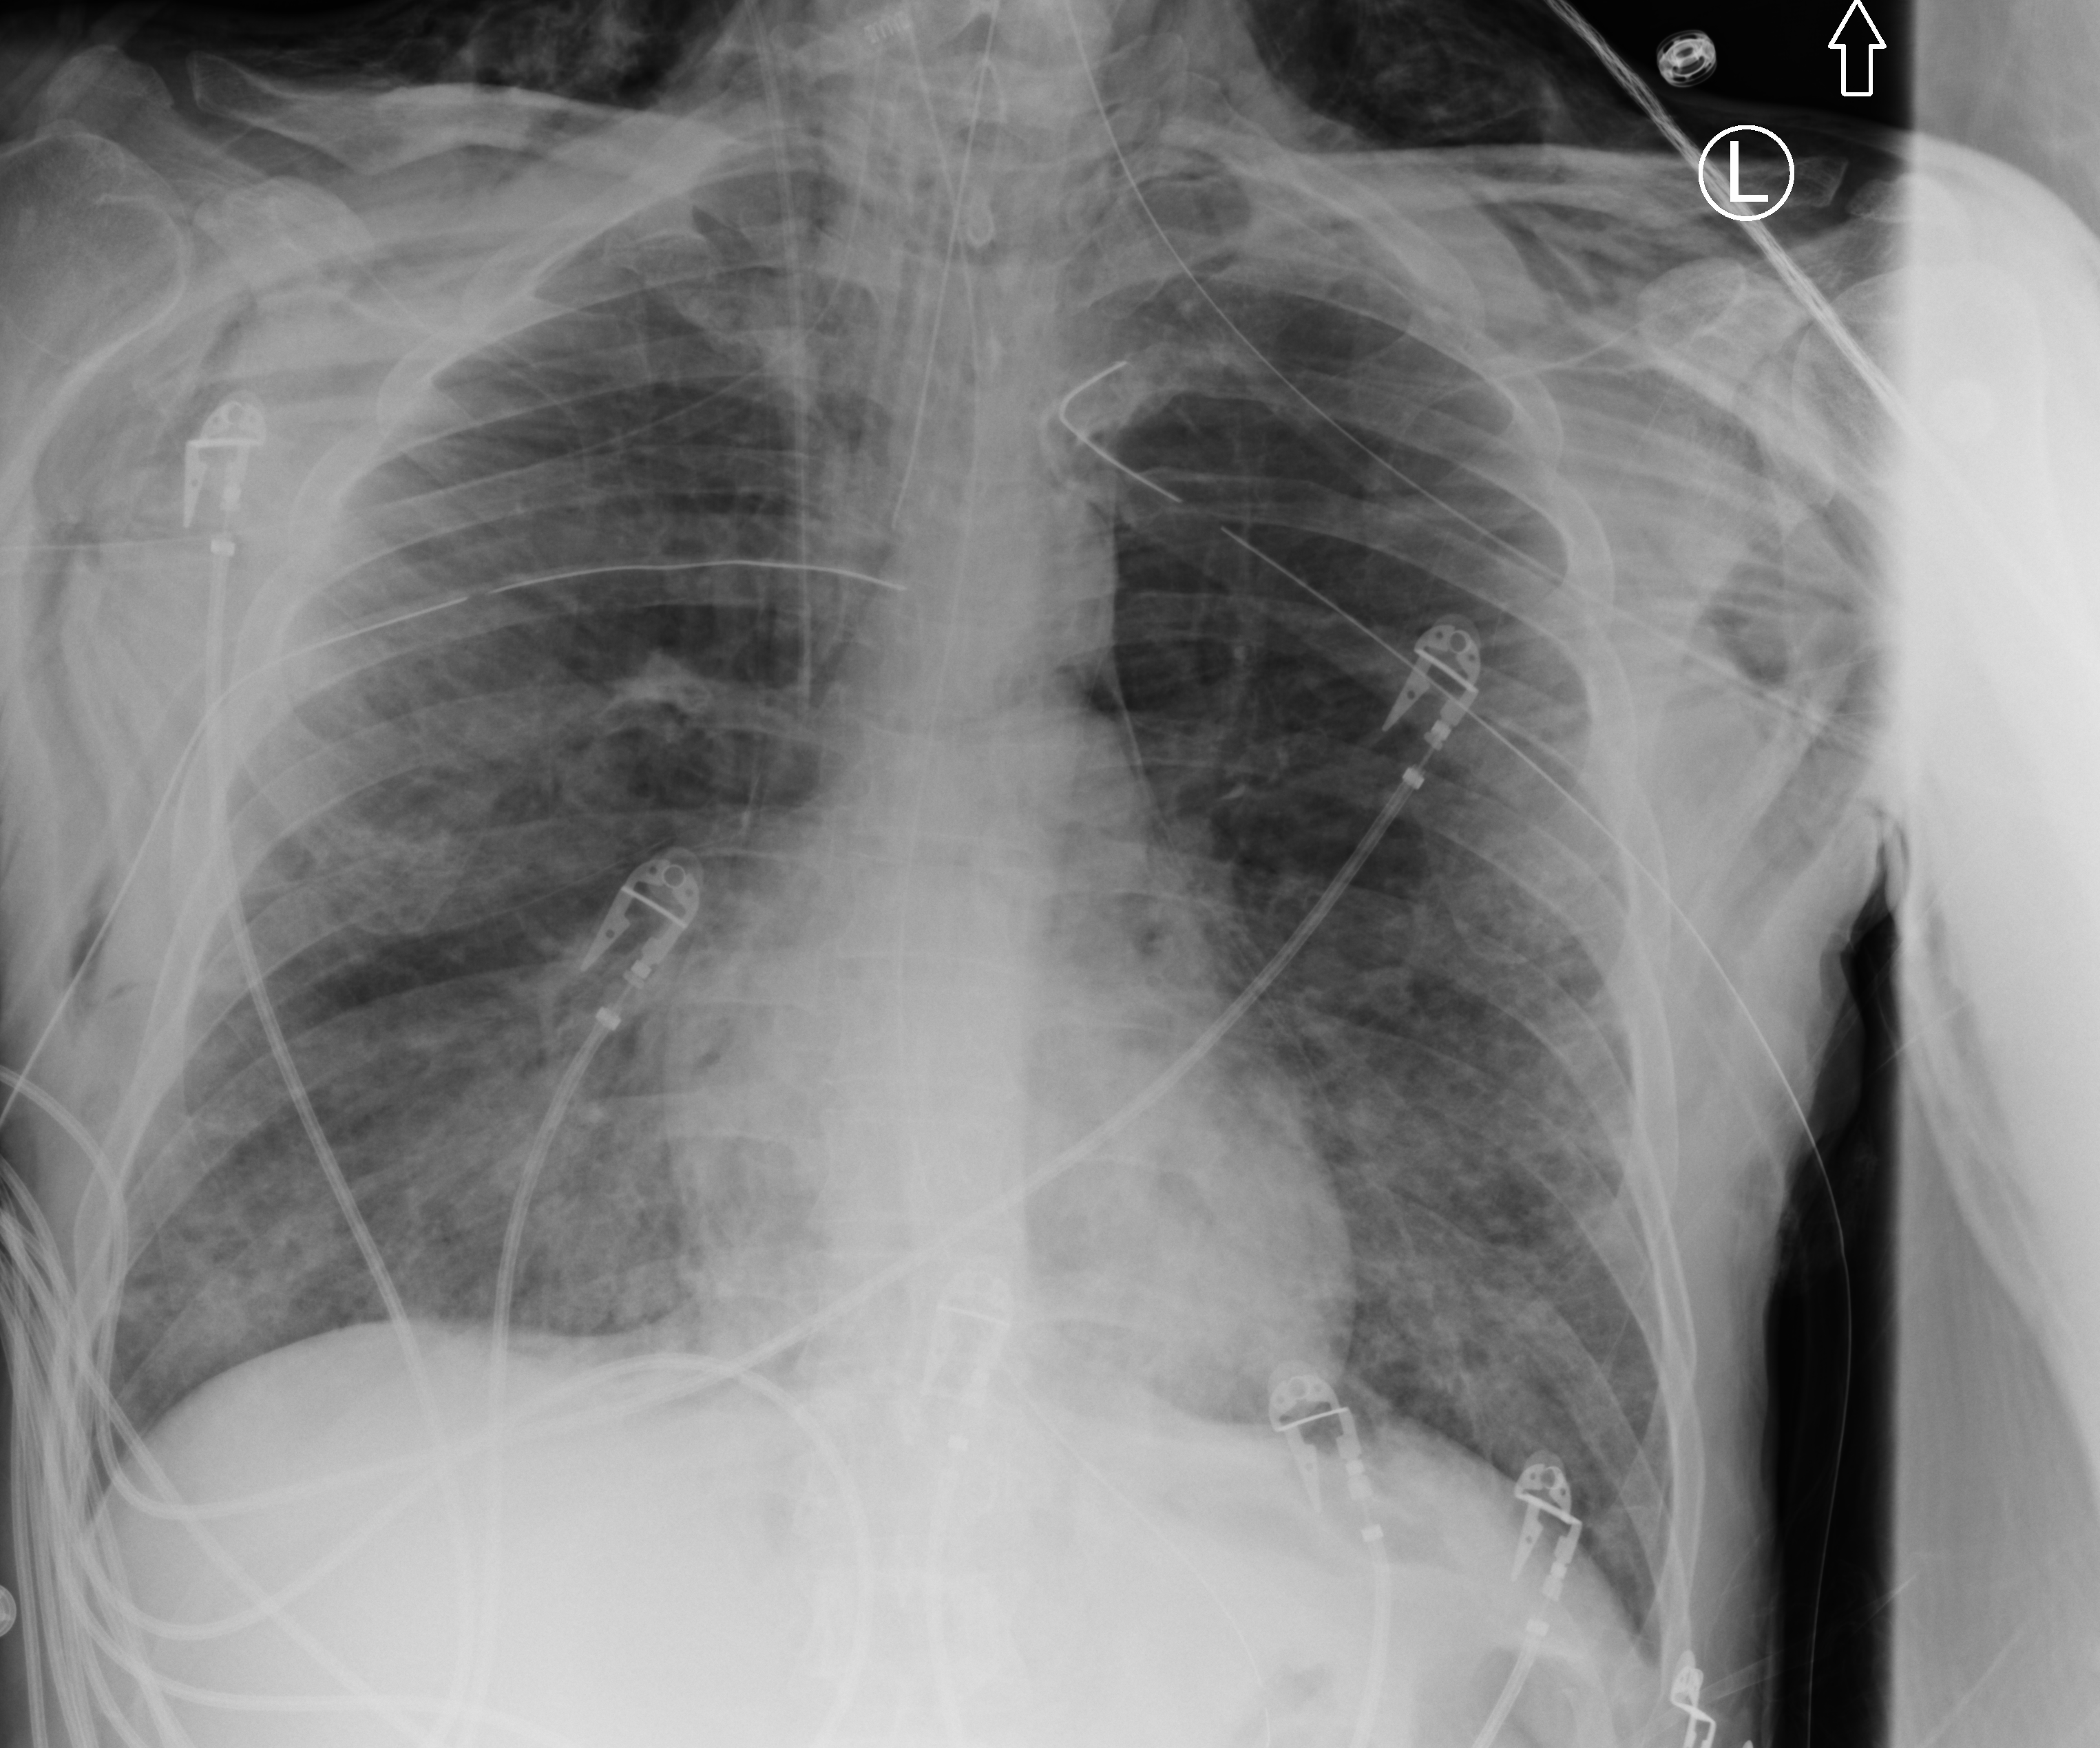
Portable chest radiograph, anteroposterior (AP) projection. Male patient hospitalised with COVID-19, age 18–59 years.
From the hospital-stay record, not from the radiograph (when in the stay this image was taken is not recorded): COPD (admission record): no; chronic kidney disease (admission record): no.